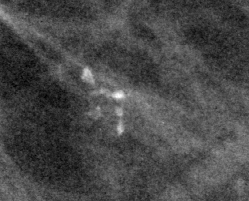
Crop from a digitized film mammogram around one marked abnormality; left breast; MLO view.
Calcifications, morphology pleomorphic, distribution regional; BI-RADS assessment category 4; pathology result (as recorded, not read from the image): benign.